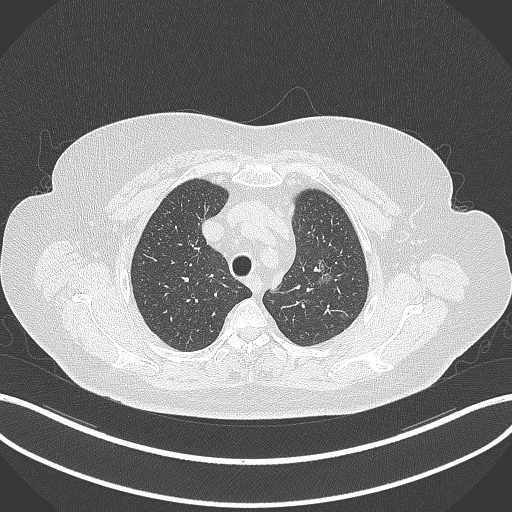
Chest CT, one axial slice; slice 270 of 309 in the series (ordered by position); lung window (W 1500 / L -600 HU); 1 mm slice thickness; 512 × 512 image matrix. Female patient, age 70 years. From the clinical record (not read from this slice): clinical TNM (as recorded): T1c N0 M0.
Structures marked on this image (bounding box drawn by a radiologist):
- lung tumour (recorded histology: adenocarcinoma): bounding box [x1, y1, x2, y2] px = [311, 257, 338, 289]